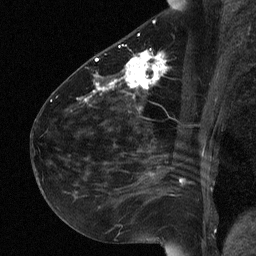
Breast MRI (dynamic contrast-enhanced), one sagittal slice; slice 33 of 64 in the series (ordered by position); dynamic contrast-enhanced study with each time point stored as its own series, time point 2 of 3 at this slice position (early post-contrast, ordered by acquisition time); 1.5 T; TE 4.8 ms, TR 27 ms; 2 mm slice thickness; 256 × 256 image matrix, field of view 180 × 180 mm. Patient: female, 51 years. From the clinical record (not read from this slice): setting: breast cancer imaged before/during neoadjuvant chemotherapy; receptor status: HR-positive, HER2-negative.
Annotated regions visible in this slice (semi-automatic segmentation, software-assisted and operator-edited):
- analysis volume of interest (the breast-tissue region the enhancement analysis was run in; not a lesion): bounding box <72,34,182,118> (left, top, right, bottom; pixels)
- tumour enhancement mask (voxels above the 90 % enhancement threshold inside the analysis volume of interest): <86,52,165,101>